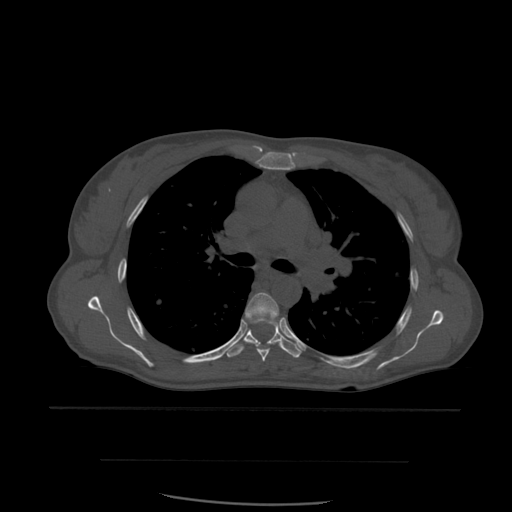
CT including the spine, one axial slice. Slice 401 of 574 in the series (ordered by position). Bone window (W 1800 / L 400 HU). 1.25 mm slice thickness. 512 × 512 image matrix, field of view 392 × 392 mm. Patient age 48 years. From the clinical record (not read from this slice): primary cancer: lung; vertebrae with lytic lesions (as recorded): T11.
Outlined on this slice (semi-automatically segmented with operator editing):
- T5 vertebra: bounding box [x1, y1, x2, y2] px = [245, 292, 282, 362]
- T6 vertebra: [225, 321, 302, 358]